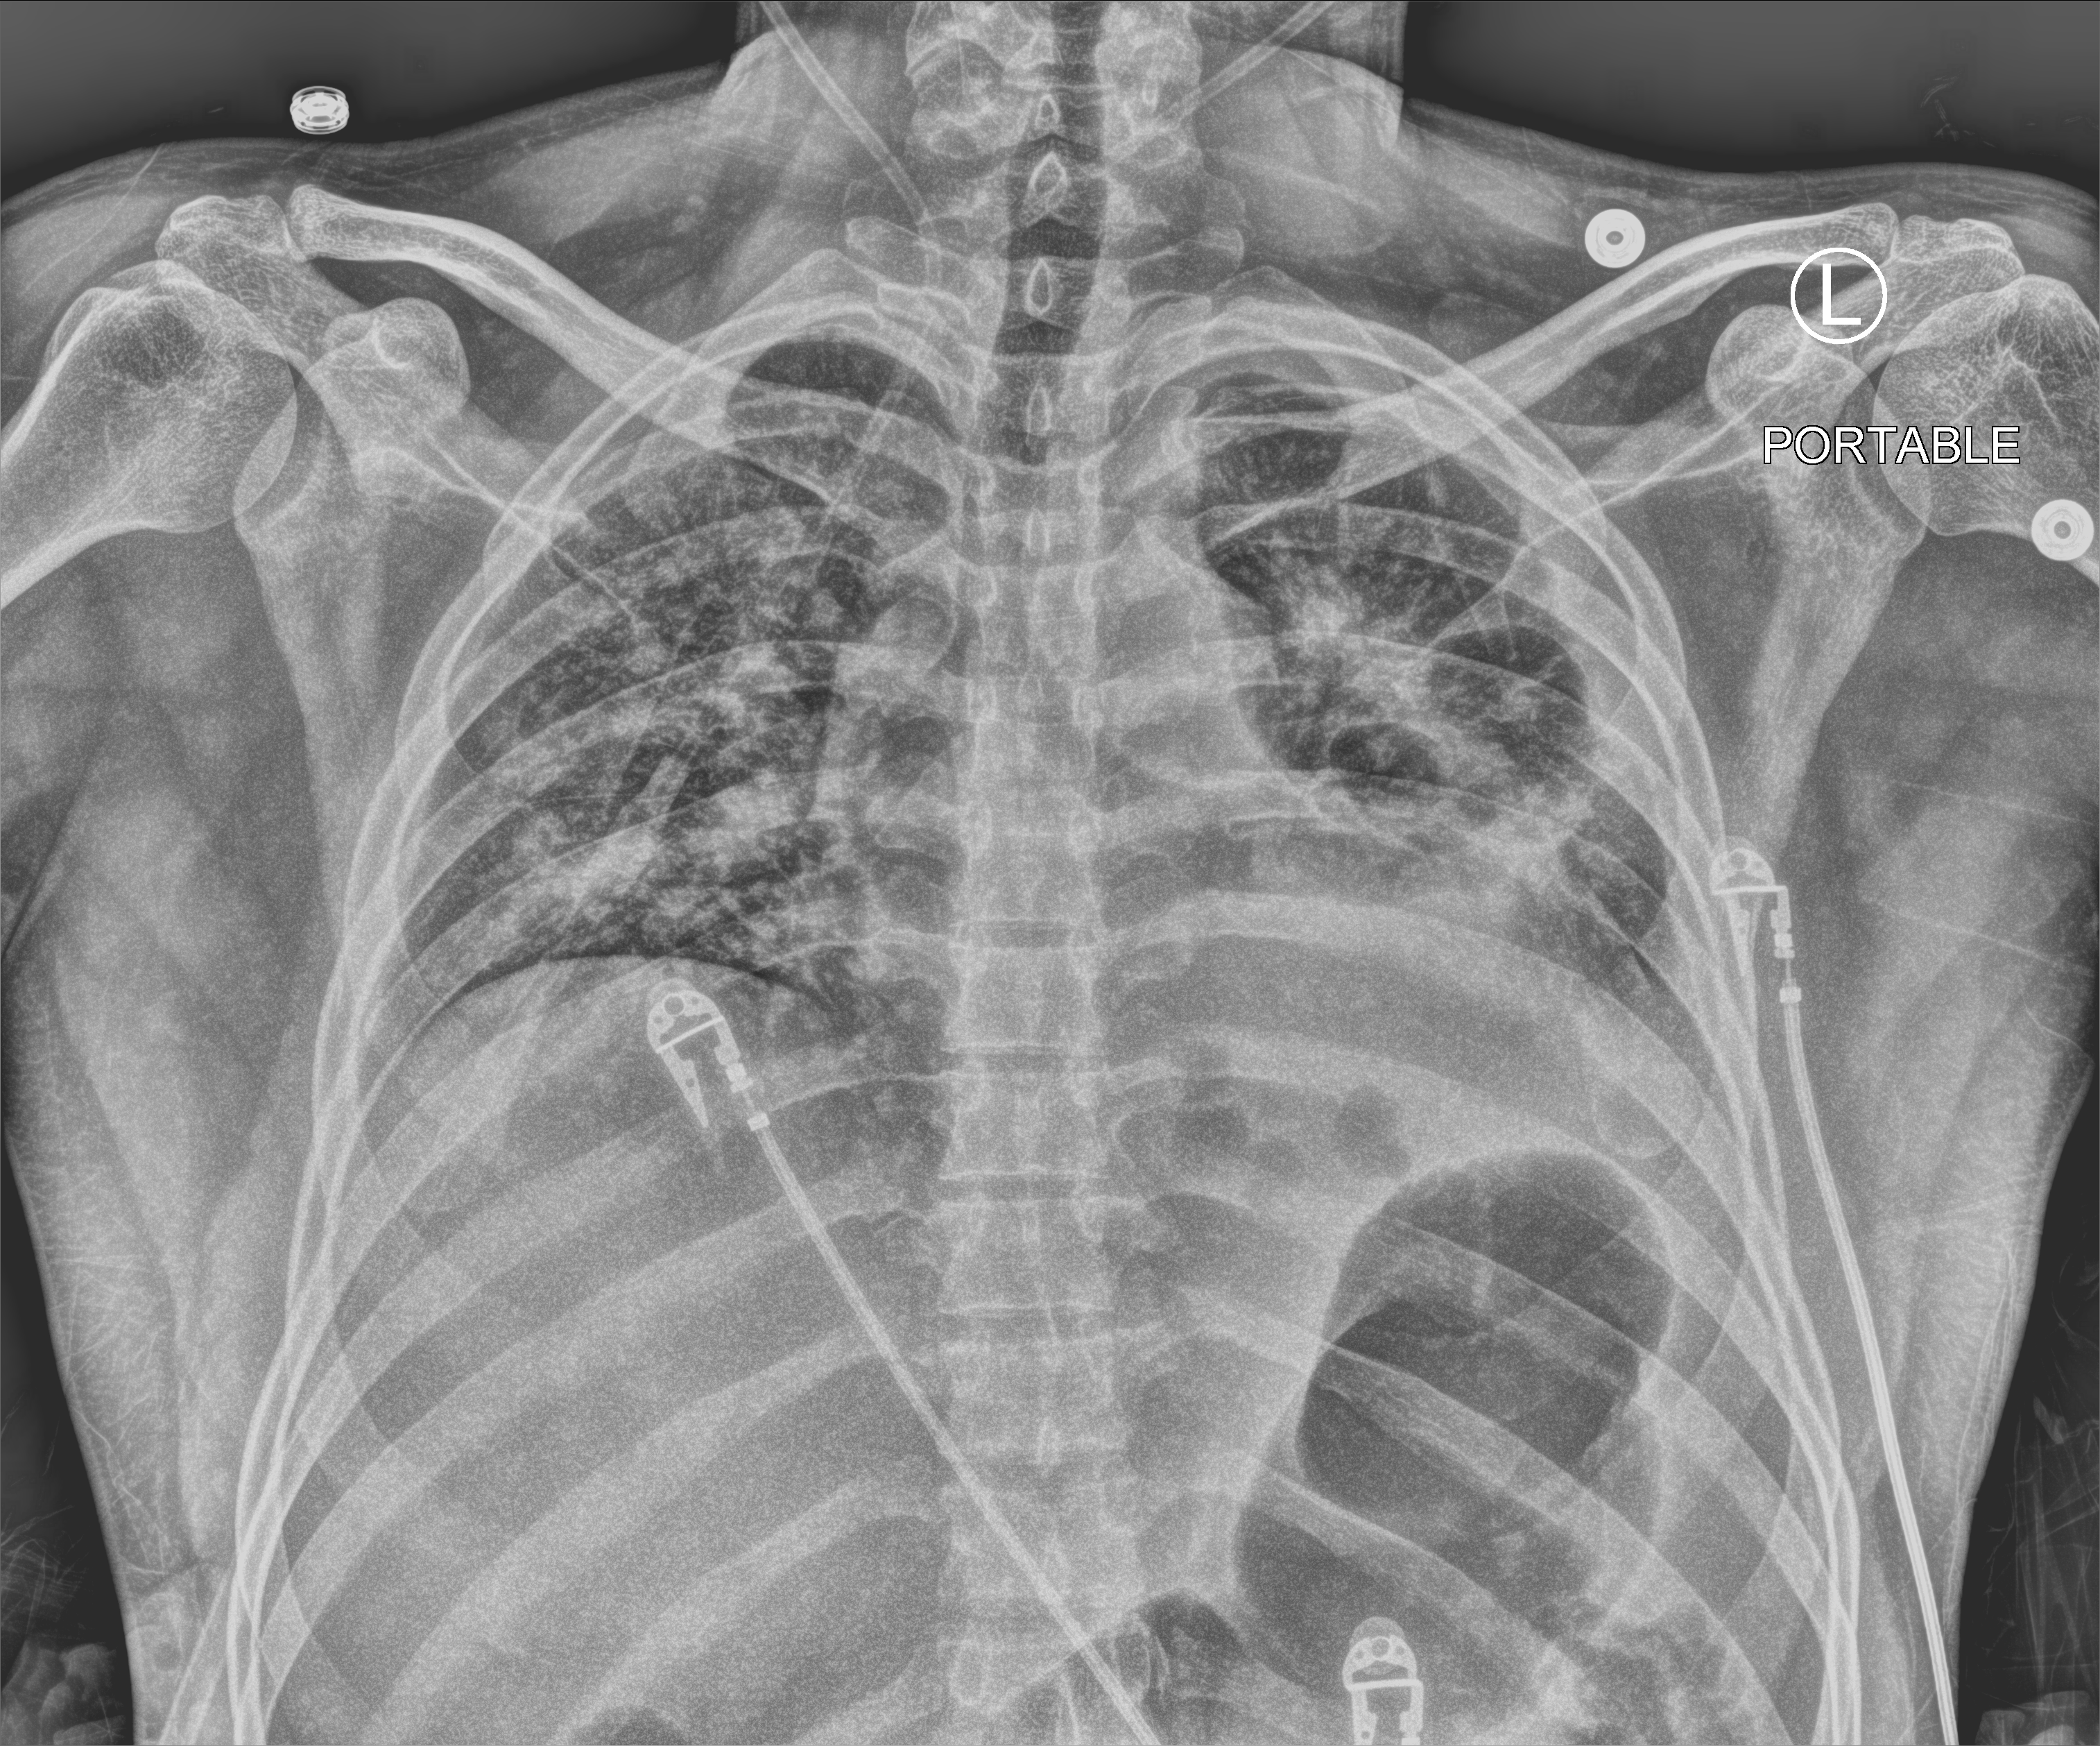
Portable chest radiograph, anteroposterior (AP) projection. Patient hospitalised with COVID-19; male, aged 18–59 years.
Hospital-stay facts (about this admission, not read from this image; timing relative to this image not recorded):
- mechanically ventilated during this hospital stay: yes
- other chronic lung disease (admission record): no
- length of hospital stay: 31 days